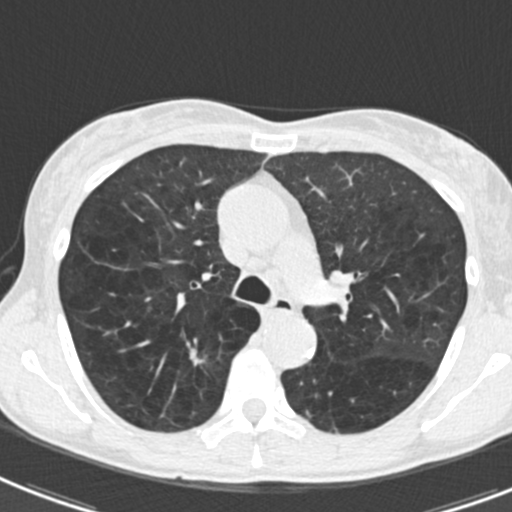
Low-dose screening chest CT, axial slice. Second screening round (one year after baseline). Lung window (W 1500 / L -600 HU). Slice 59 of 186 in the series. 512 × 512 image matrix. Female participant, aged 61 years at enrolment. Current smoker at enrolment.
Expert reader's lesion annotation, bounding box [x1, y1, x2, y2] px = [167, 331, 224, 376]. The exam's reader record, not a measurement of the box and not confirmed to be the same lesion: non-calcified nodule or mass ≥4 mm, right upper lobe, 12 × 6 mm, smooth margins, soft tissue attenuation, pre-existing on the prior screen: yes; interval growth: yes. Lung cancer was diagnosed 455 days after this screen: non-small cell carcinoma, right upper lobe, undifferentiated (G4), stage IA (AJCC 6th edition), 15 mm at pathology.